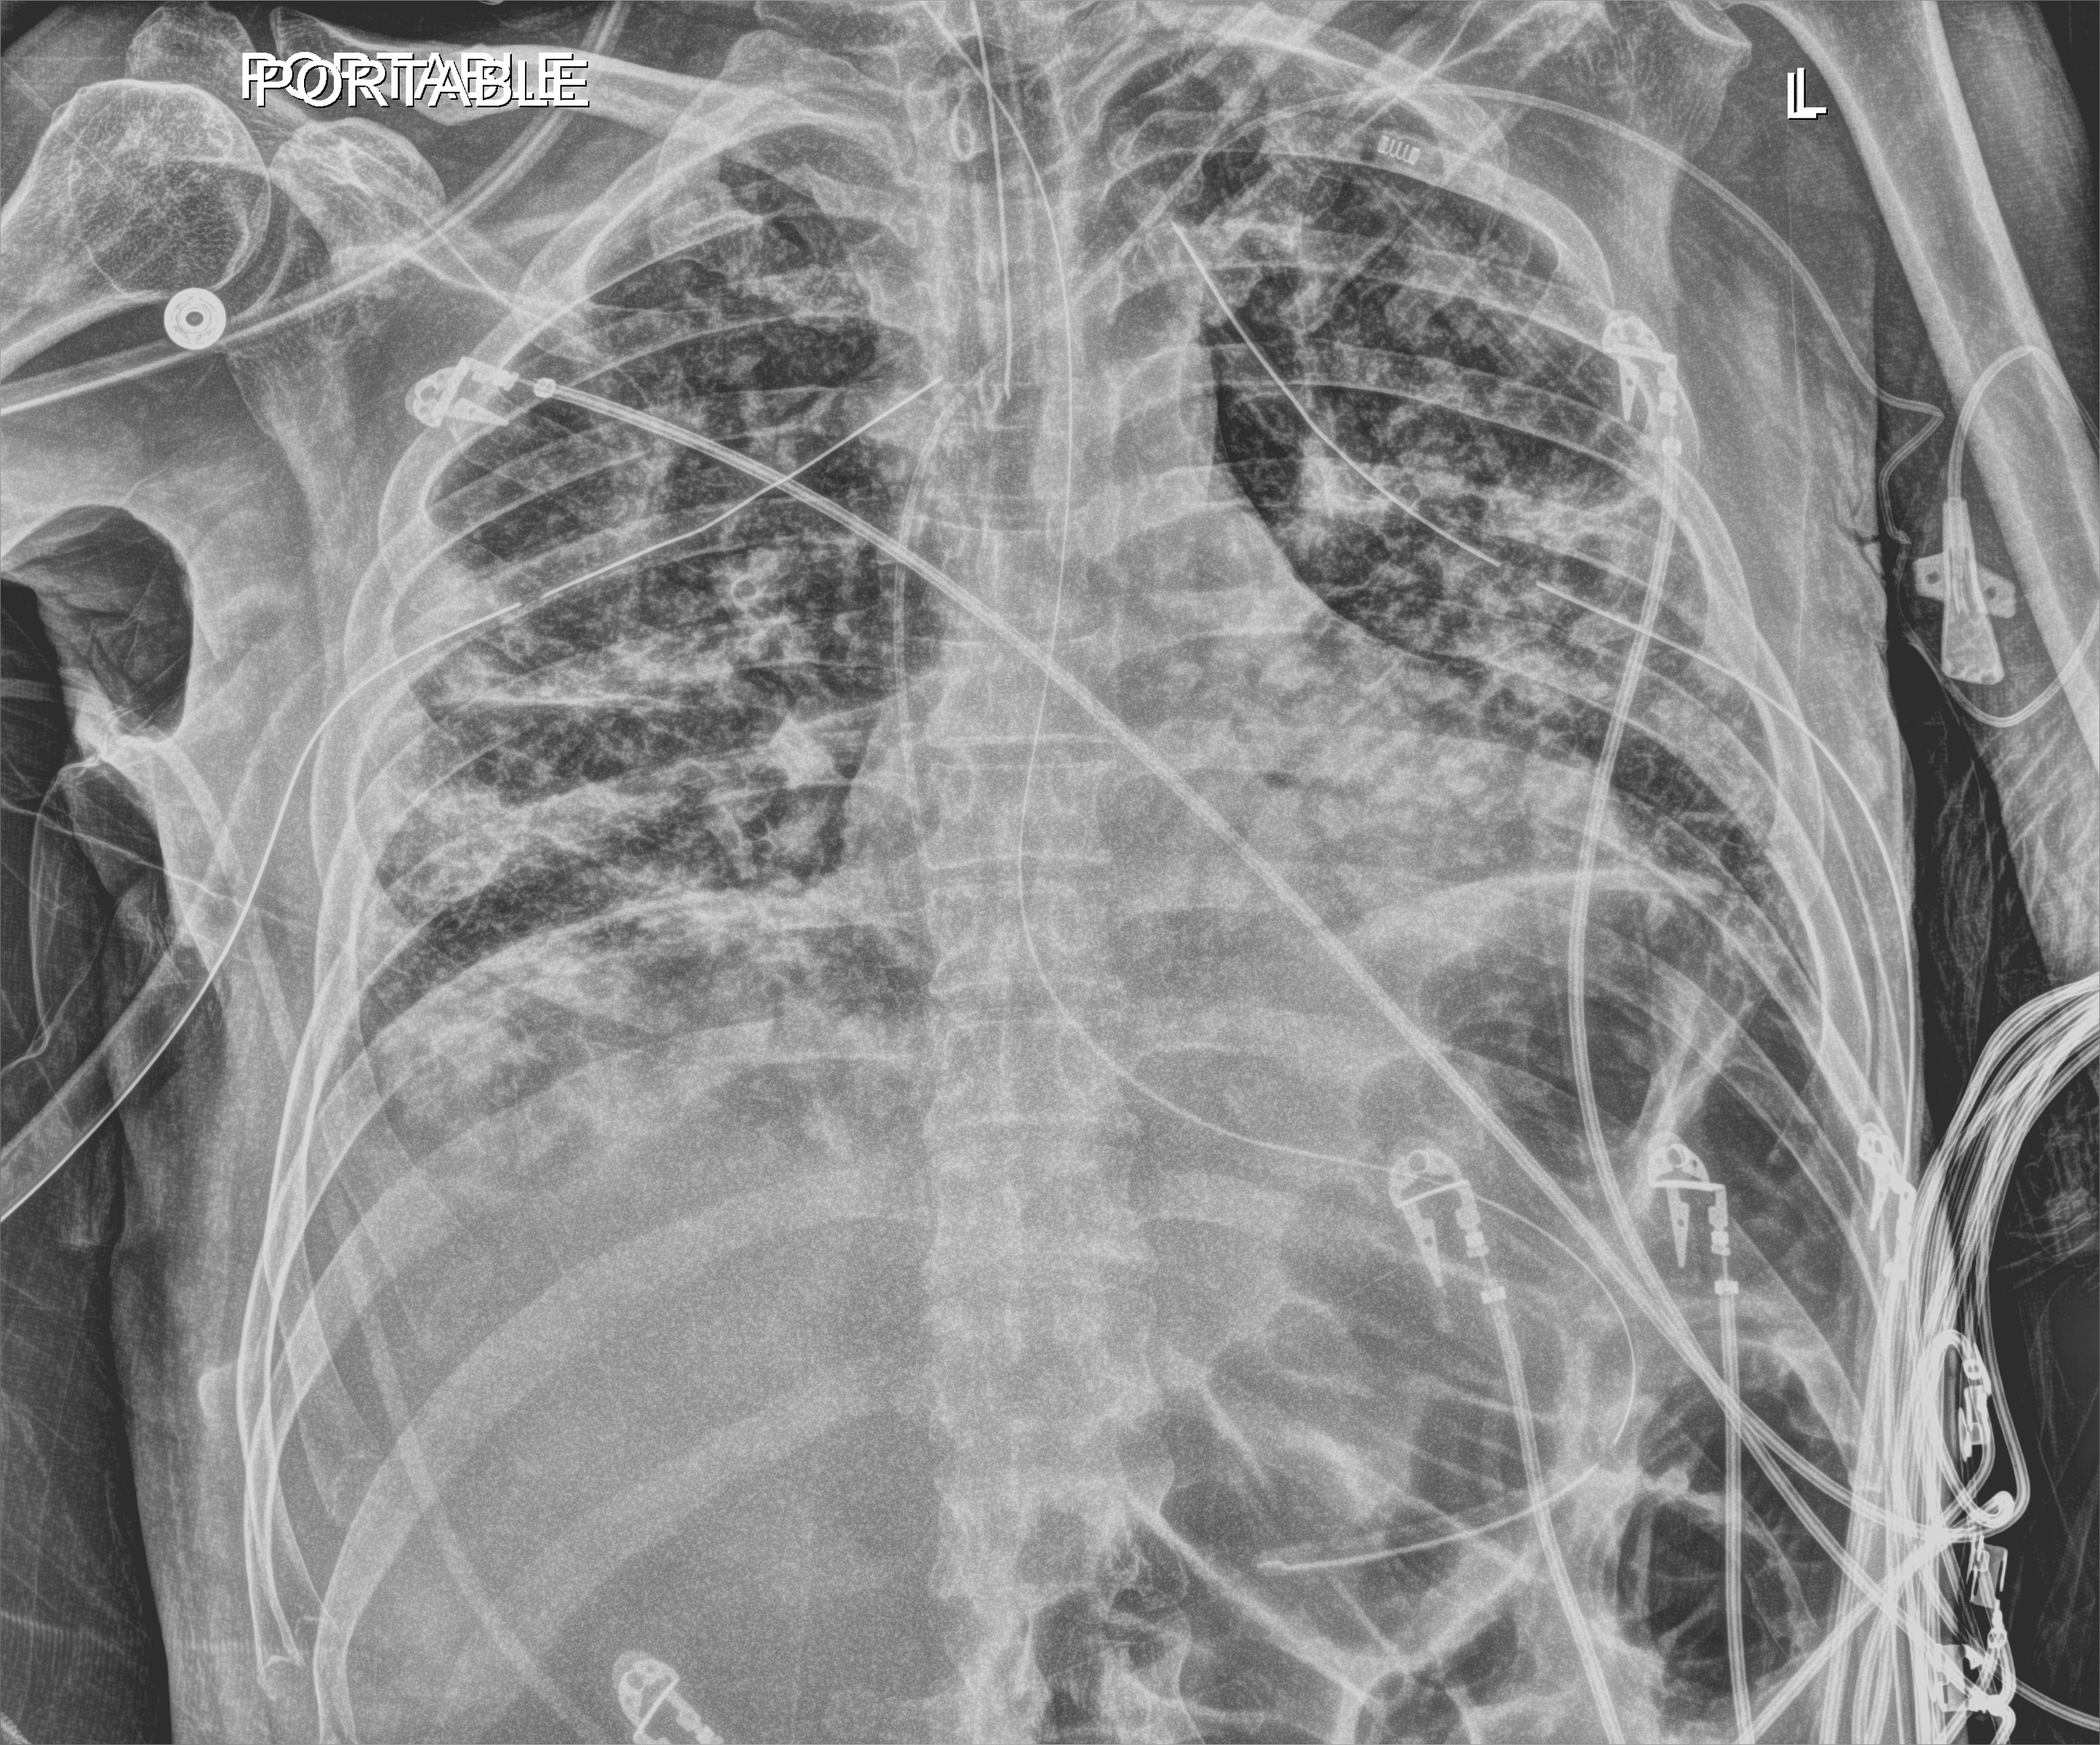
Portable chest radiograph, anteroposterior (AP) projection. Male patient hospitalised with COVID-19, age 18–59 years.
From the hospital-stay record, not from the radiograph (when in the stay this image was taken is not recorded):
- mechanically ventilated during this hospital stay: yes
- length of hospital stay: 96 days